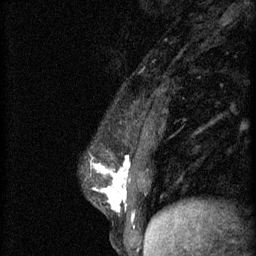
Breast MRI (dynamic contrast-enhanced), one sagittal slice. Slice 18 of 60 in the series (ordered by position). 3 images stored at this slice position (order not interpretable as contrast timing). 1.5 T. TE 4.2 ms, TR 11 ms. 2 mm slice thickness. 256 × 256 image matrix, field of view 180 × 180 mm. Patient: female, 37 years.
Structures marked on this image (semi-automatically segmented with operator editing):
- analysis volume of interest (the breast-tissue region the enhancement analysis was run in; not a lesion): bounding box [x1, y1, x2, y2] px = [90, 142, 174, 221]
- tumour enhancement mask (voxels above the 70 % enhancement threshold inside the analysis volume of interest): [91, 158, 130, 213]